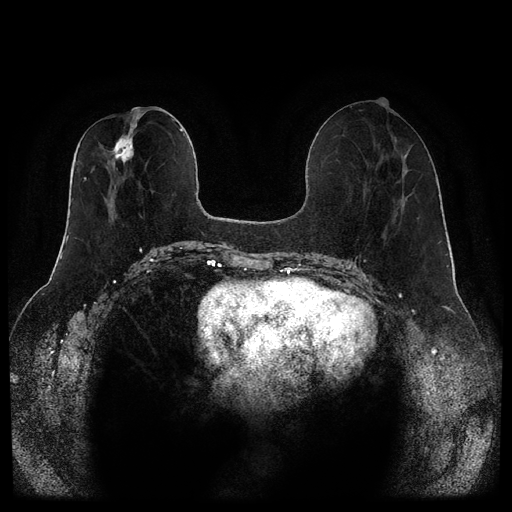
Breast MRI (dynamic contrast-enhanced, multi-phase), one axial slice. Position 44 of 116 along the scan axis. Dynamic contrast-enhanced series, time point 2 of 5 at this slice position (early post-contrast). 1.5 T. TE 2.6 ms, TR 5.3 ms. 512 × 512 image matrix, field of view 350 × 350 mm. Female patient, age 46 years.
Structures marked on this image (semi-automatically segmented with operator editing):
- breast lesion (labelled 'tumour' in the annotation; benign lesions carry a separate 'benign' label): bounding box [x1, y1, x2, y2] px = [112, 119, 138, 165]